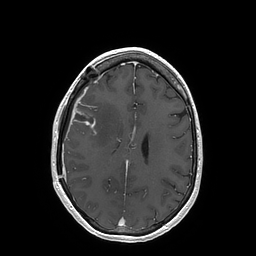
Brain MRI from a brain-tumour surgery series, one axial slice. Slice 65 of 202 in the series (ordered by position). T1-weighted post-contrast. 1 mm slice thickness. 256 × 256 image matrix, field of view 250 × 250 mm. From the clinical record (not read from this slice): histopathology: Glioblastoma; WHO grade: 4; IDH mutation: no.
Outlined on this slice (outlined manually by an expert reader):
- tumour: bounding box (x1, y1, x2, y2) in pixels: (72, 108, 96, 134)